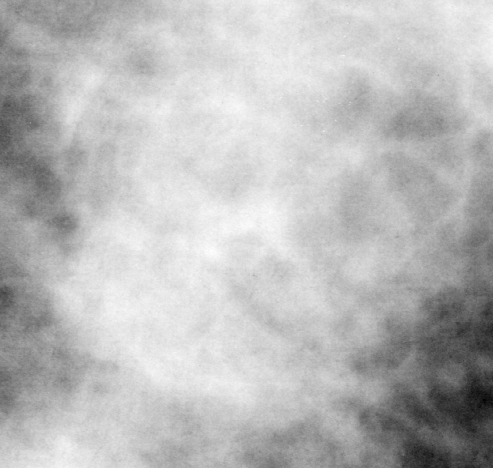
Region of interest cut from a scanned film mammogram (one marked finding); left breast; MLO view.
- Mass, shape architectural distortion, margins ill defined; BI-RADS assessment category 5; pathology (as recorded): malignant.